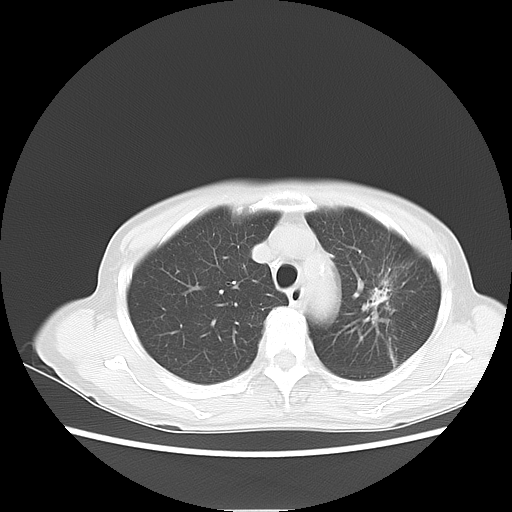
Chest CT, one axial slice. Position 7 of 13 along the scan axis. Reconstruction kernel LUNG. 120 kVp. Lung window (W 1500 / L -600 HU). 5 mm slice thickness. 512 × 512 image matrix, field of view 350 × 350 mm. Patient: female, 71 years. Case-level facts recorded for this patient, not image findings: clinical TNM (as recorded): T2 N0 M0.
Outlined on this slice (rectangle marked by the reading radiologist):
- lung tumour (recorded histology: adenocarcinoma): bounding box (x1, y1, x2, y2) in pixels: (362, 277, 394, 314)